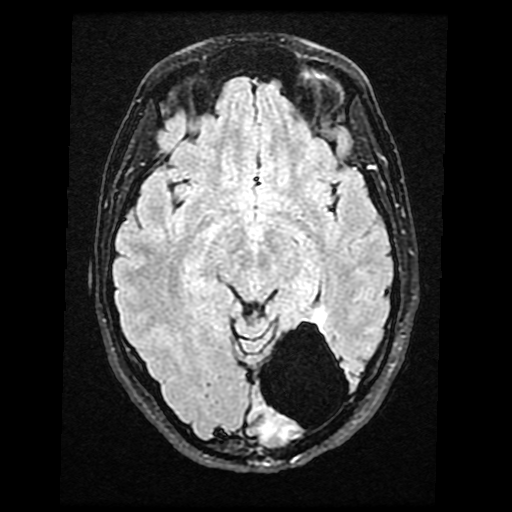
Brain MRI from a brain-tumour surgery series, one axial slice. Slice 24 of 40 in the series (ordered by position). T2 FLAIR. 4 mm slice thickness. 512 × 512 image matrix. From the clinical record (not read from this slice): histopathology: Glioma with ependymal features; WHO grade: 2; tumour location: Left Parietal.
Outlined on this slice (manually delineated by an expert):
- tumour: box from (x=280, y=307) to (x=325, y=438) px